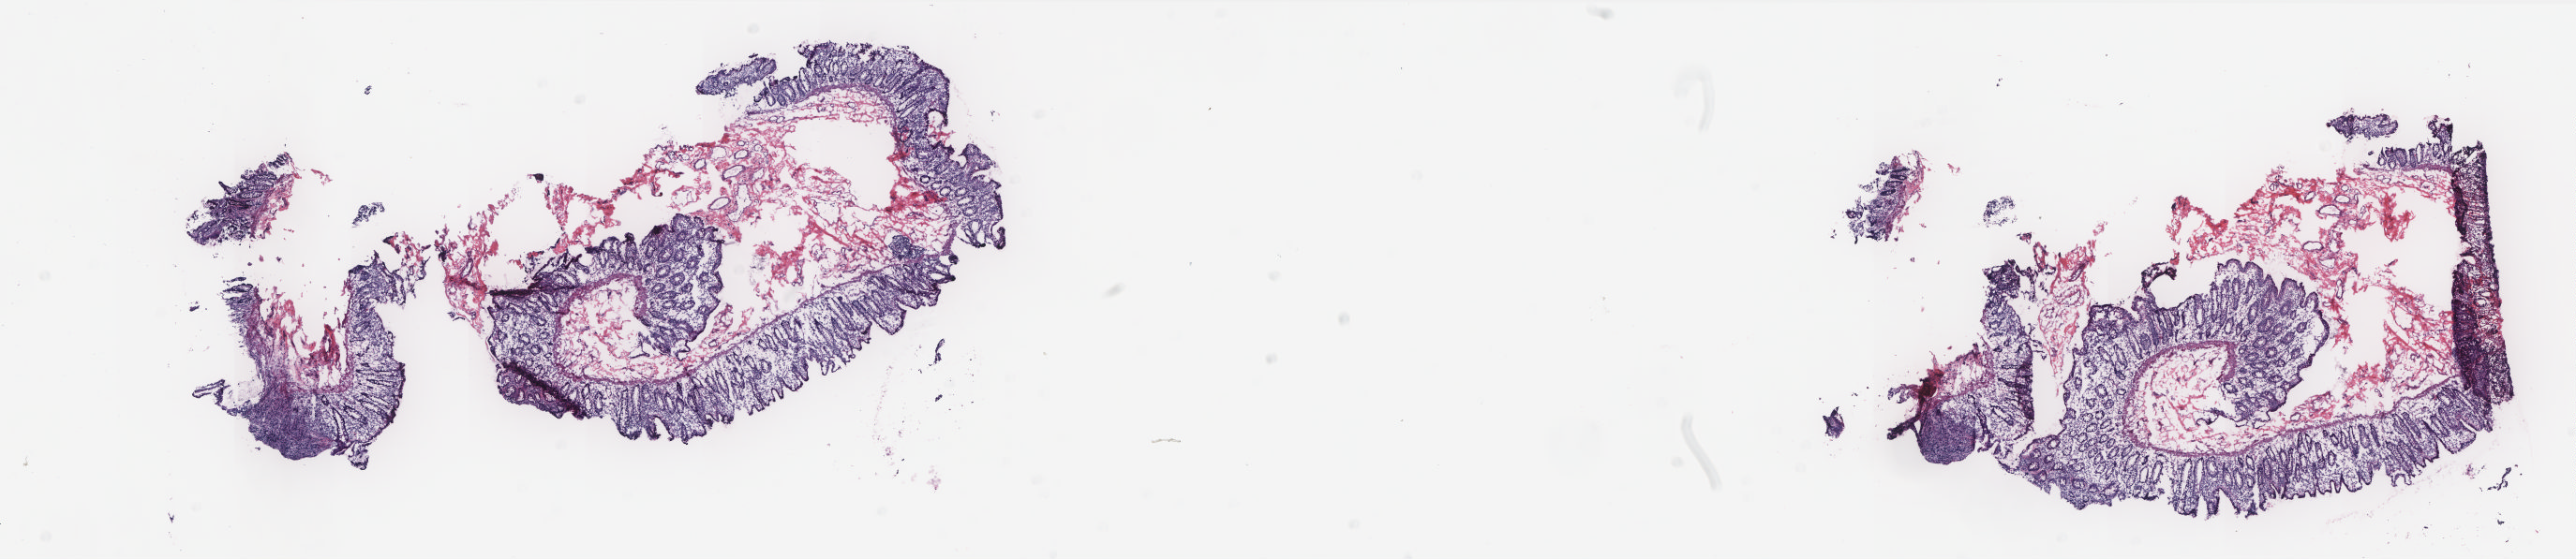
Whole-slide histology image, H&E-stained — whole scanned area (about 22.0 x 4.8 mm) shown as a low-resolution overview. Frozen section from the bottom of the tissue portion. Solid tissue normal (non-tumour tissue) sample from the colon. Female patient; age at initial diagnosis 80 years. Slide review estimates, as recorded: tumour cells 0%, normal cells 100%. Infiltration values recorded for this section: lymphocyte infiltration 40%, monocyte infiltration 8%, neutrophil infiltration 0%.
* this section: solid tissue normal sample (biorepository sample class)
* patient diagnosis: Adenocarcinoma, NOS (ascending colon)